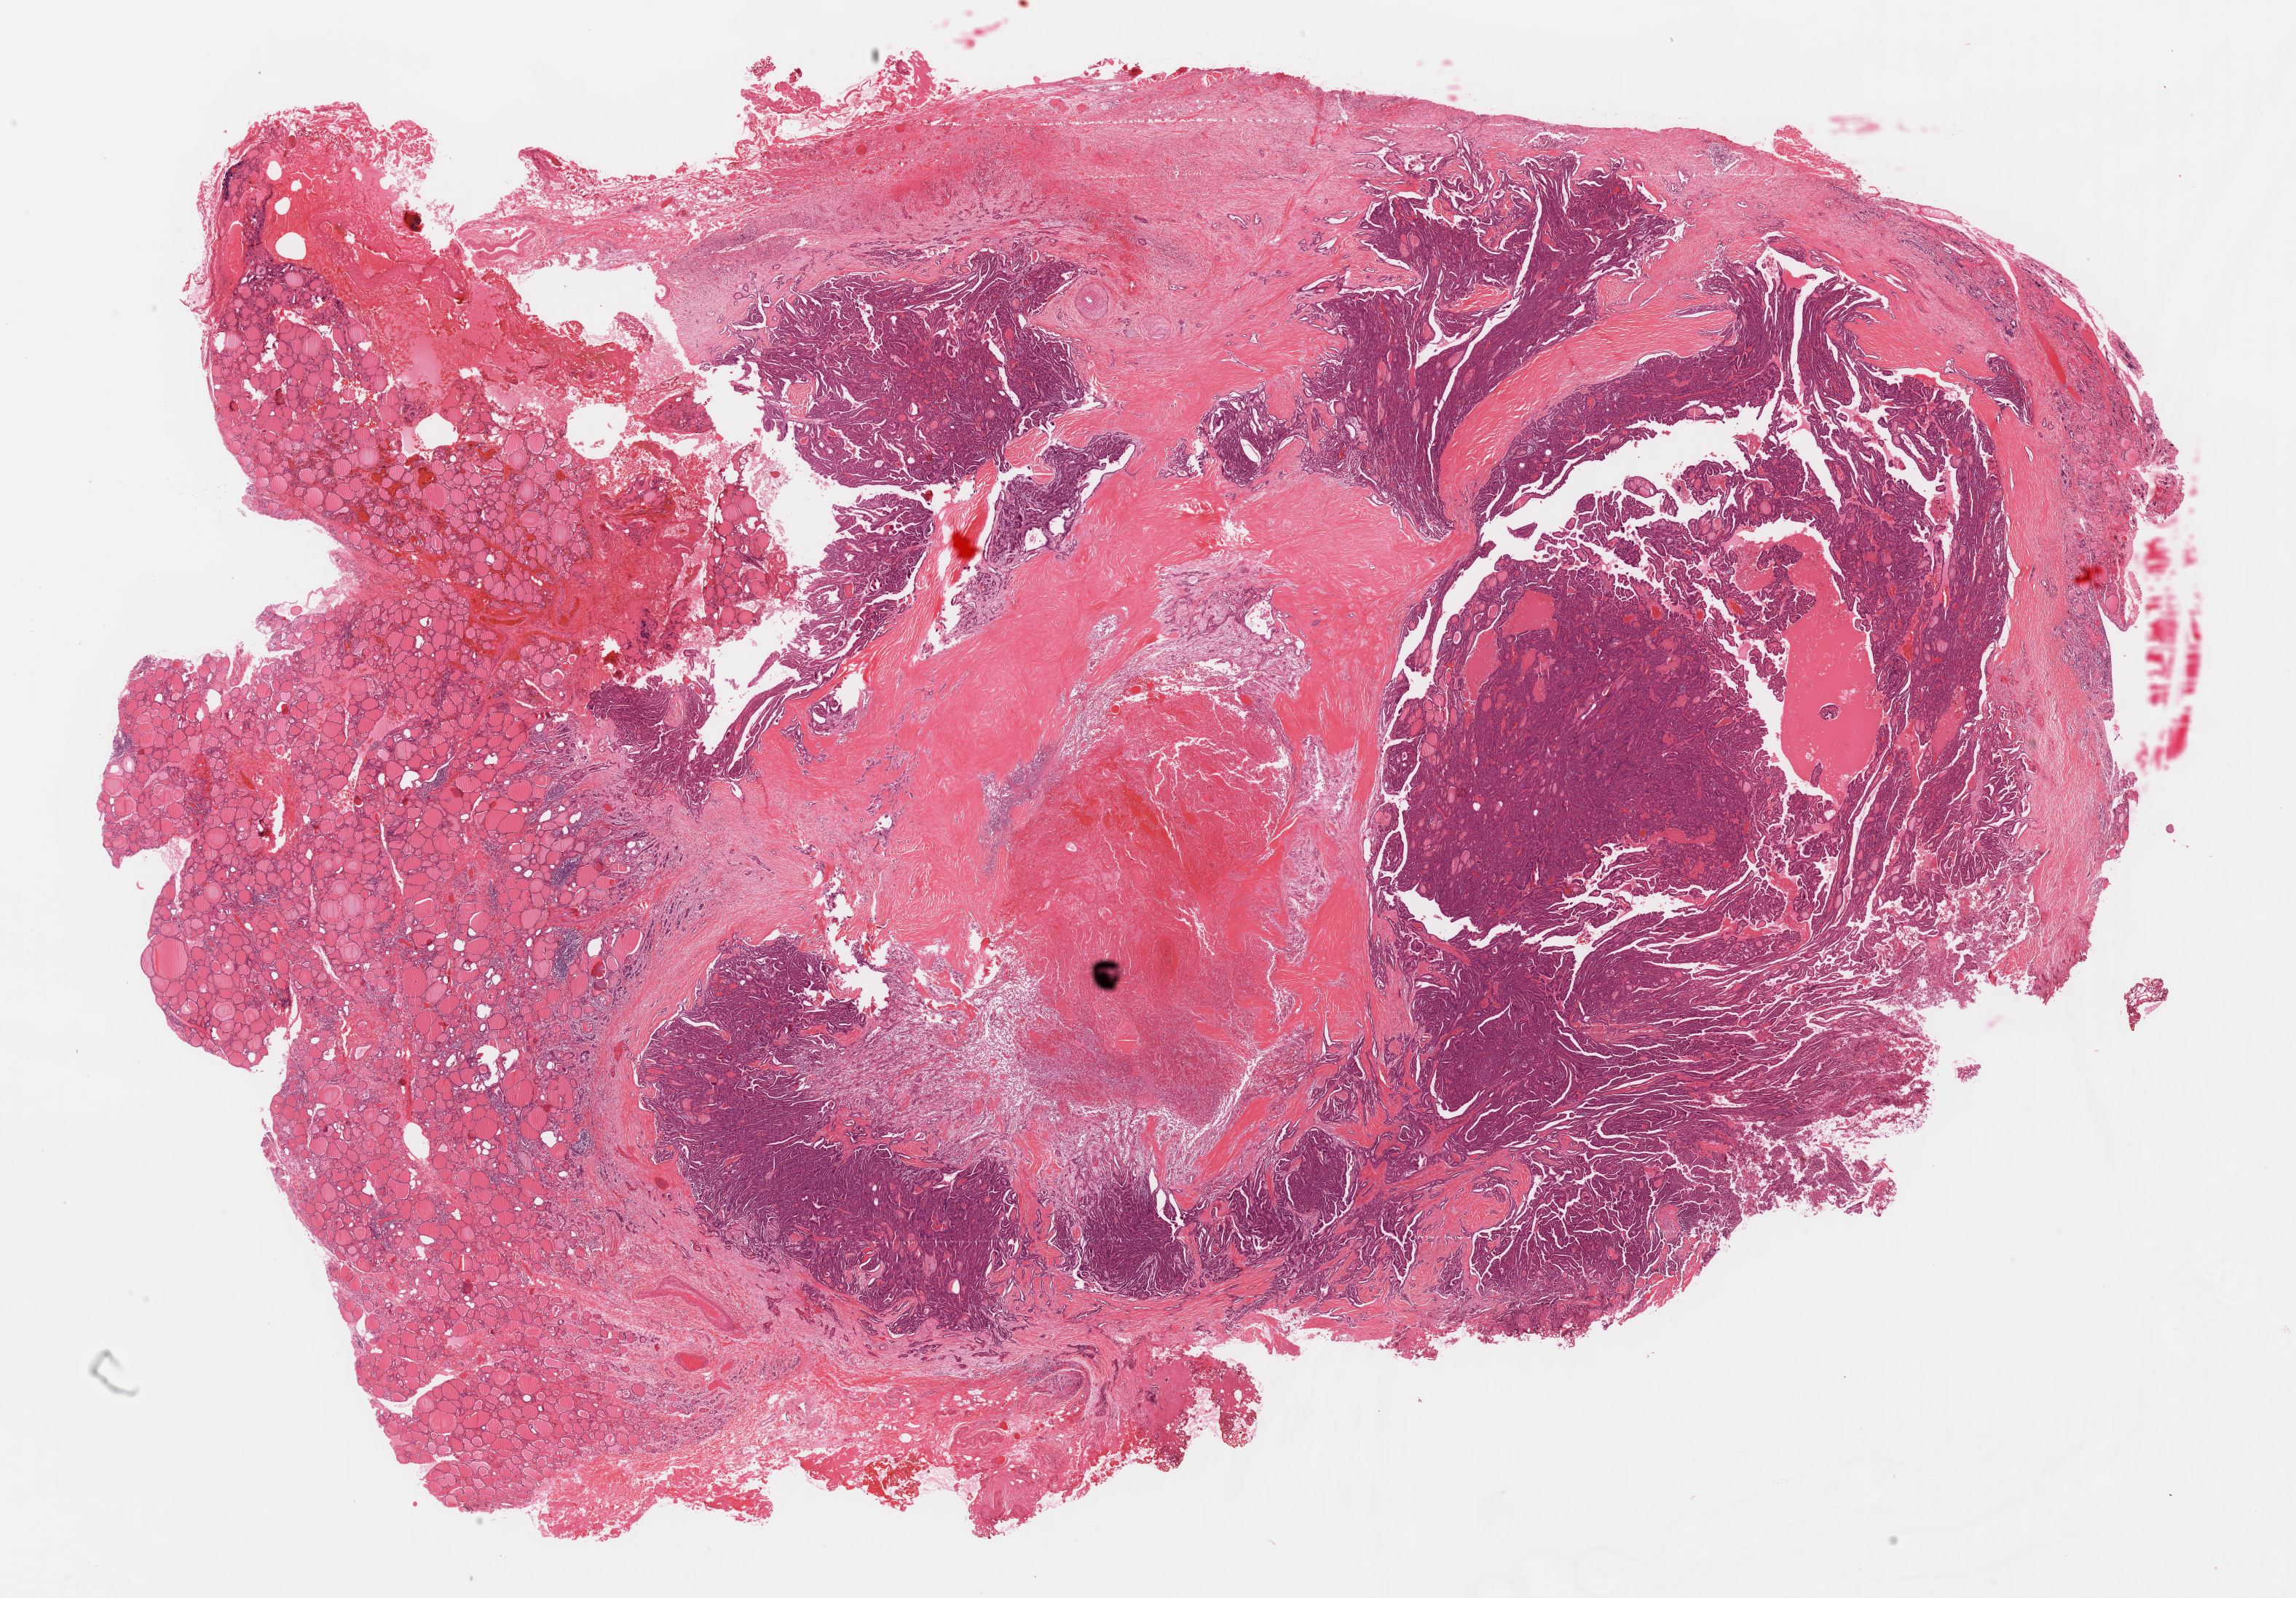
Digitized H&E tissue section (whole slide), a low-resolution overview of the entire scanned area, about 24.9 x 17.3 mm (slide scanned at 40x). Formalin-fixed paraffin-embedded (FFPE) diagnostic section. Sample: primary tumour, thyroid. Female patient; age at initial diagnosis 38 years.
* AJCC pathologic stage: I
* laterality: right
* pathologic diagnosis: Papillary adenocarcinoma, NOS (thyroid gland)